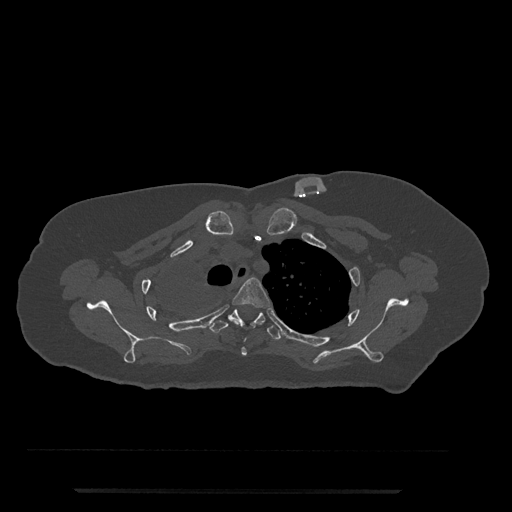
CT including the spine, one axial slice; position 613 of 797 along the scan axis; bone window (W 1800 / L 400 HU); 0.5 mm slice thickness; 512 × 512 image matrix, field of view 440 × 440 mm. Patient: female, 51 years. Case-level facts recorded for this patient, not image findings: primary cancer: neuro.
Annotated regions visible in this slice (semi-automatically segmented with operator editing):
- T3 vertebra: box from (x=232, y=277) to (x=270, y=356) px
- T4 vertebra: (x=209, y=309)–(x=281, y=340)